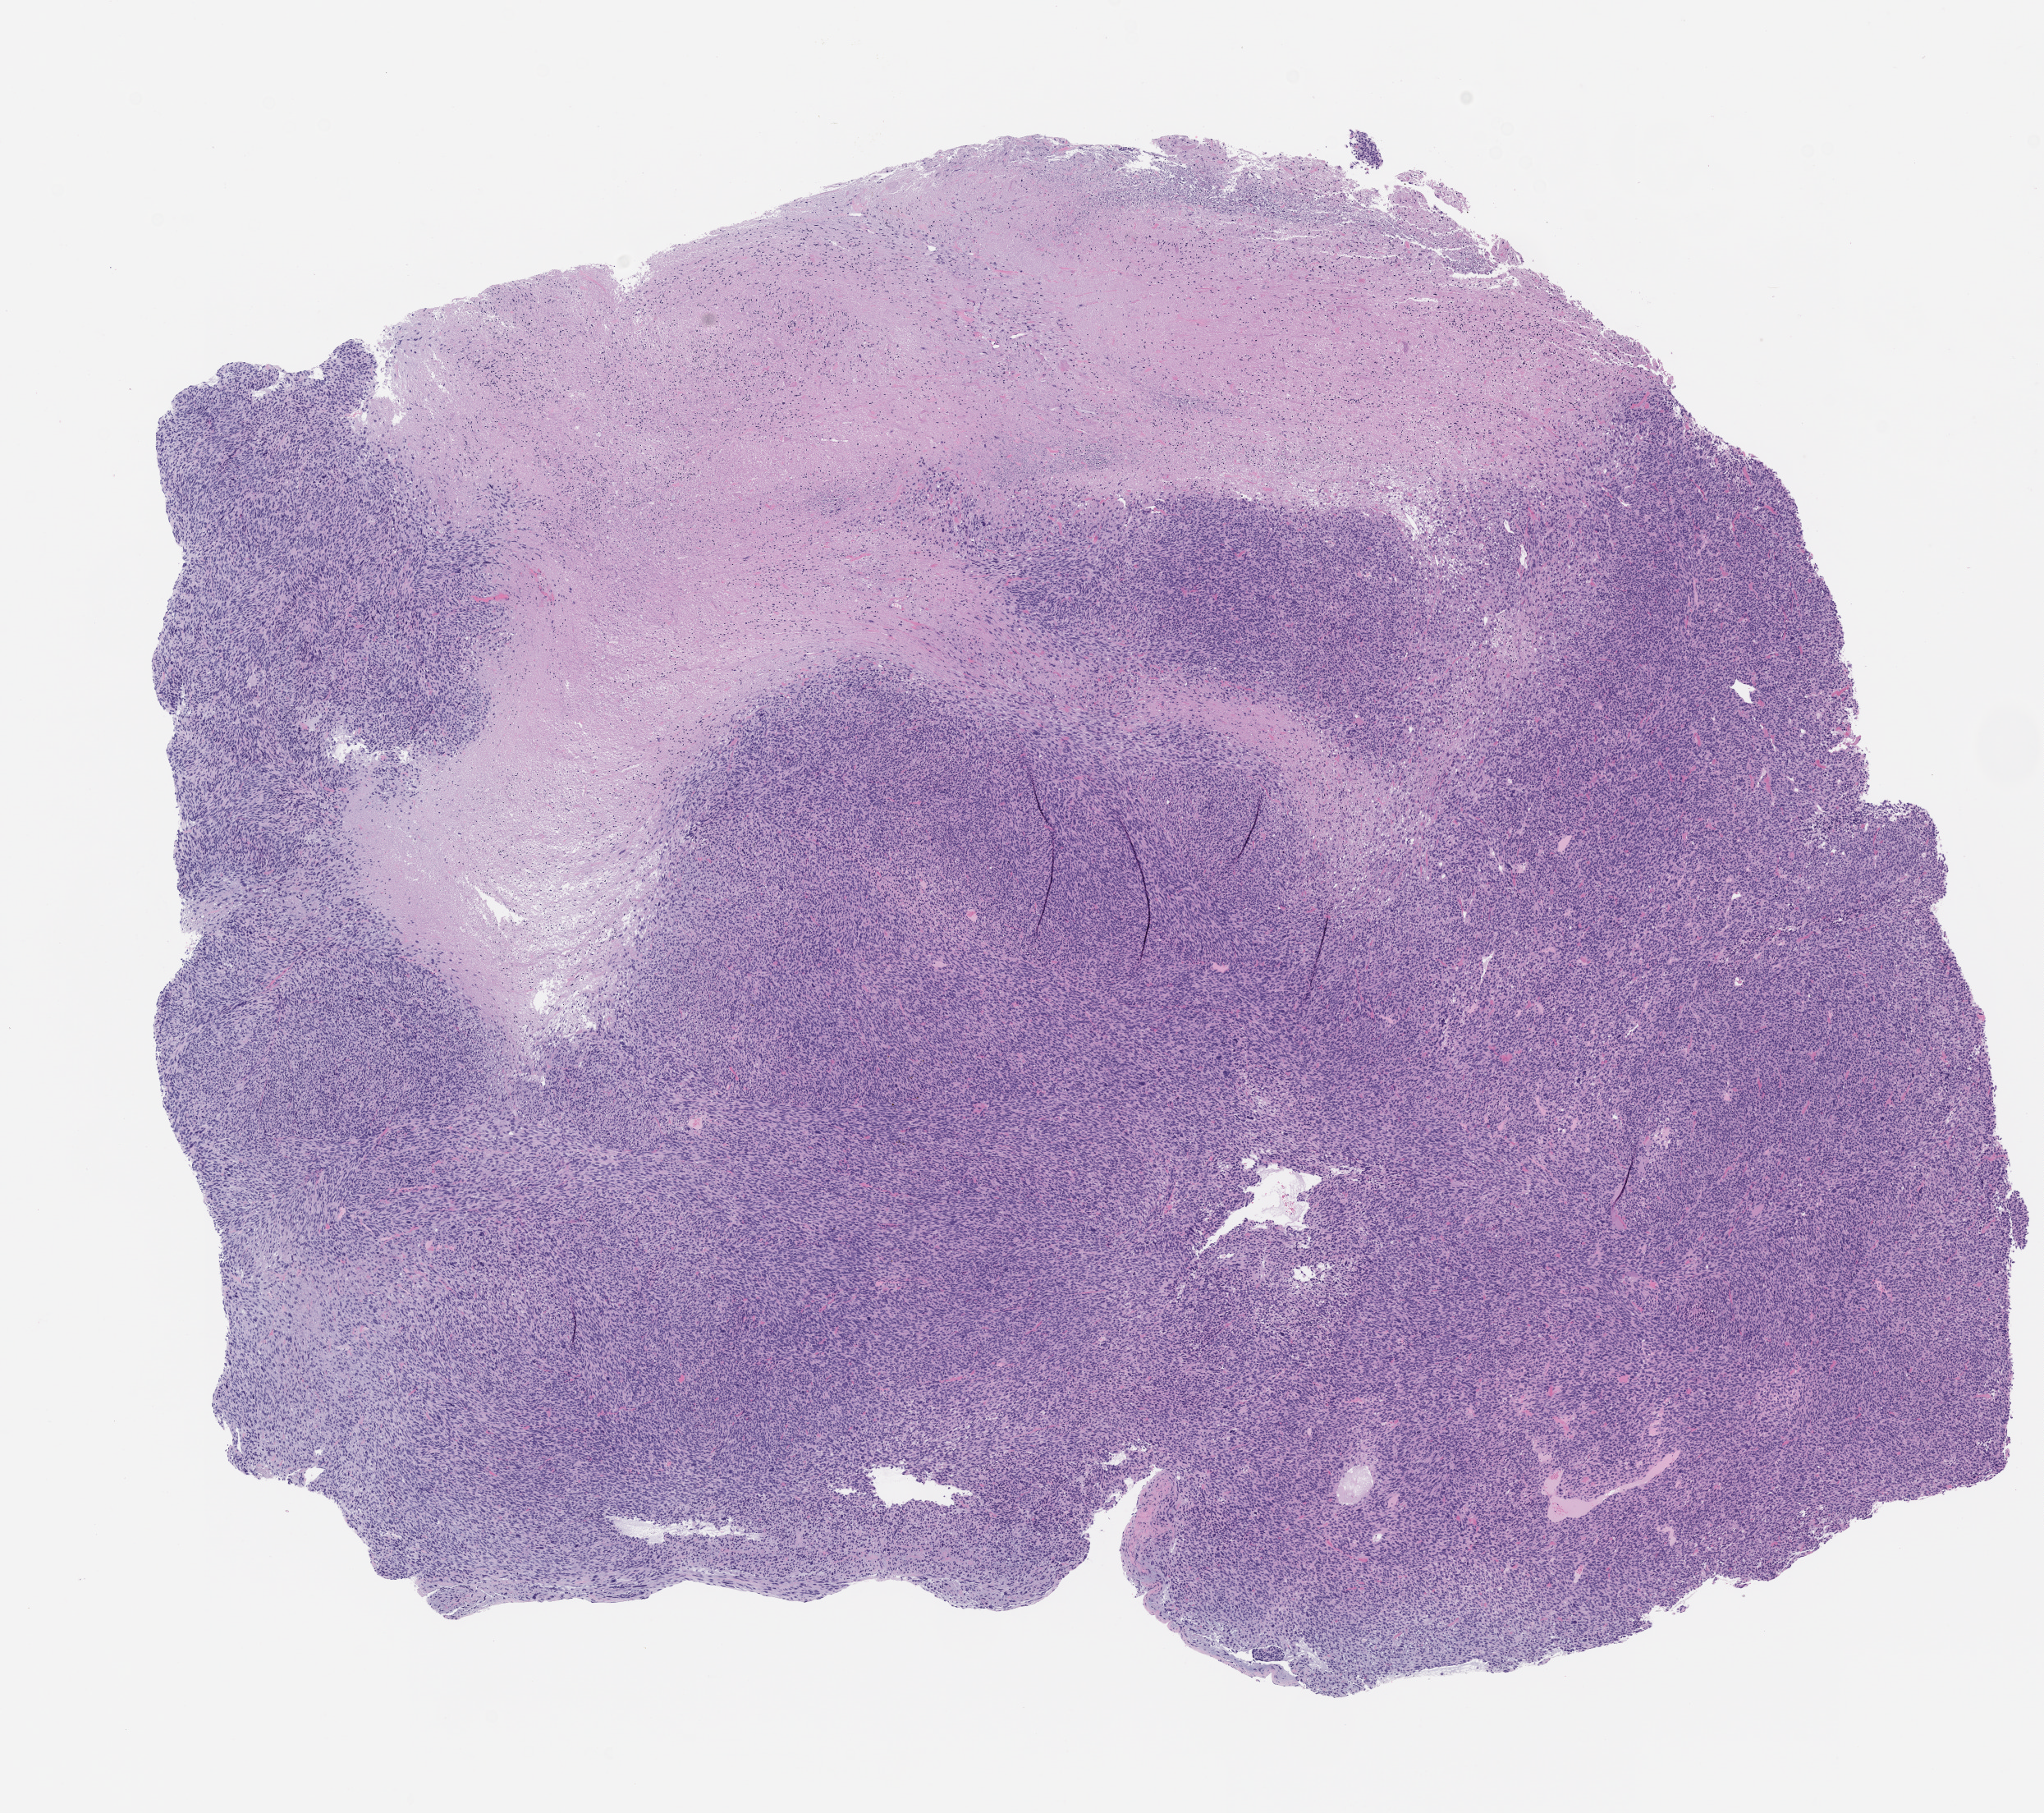
Whole-slide image, H&E: patient-derived xenograft (human tumor grown in a mouse), passage 1, whole scanned area (about 10.0 x 8.9 mm) shown as a low-resolution overview, FFPE section, originating tumor site category: uterus.
Originating patient diagnosis: Leiomyosarcoma.